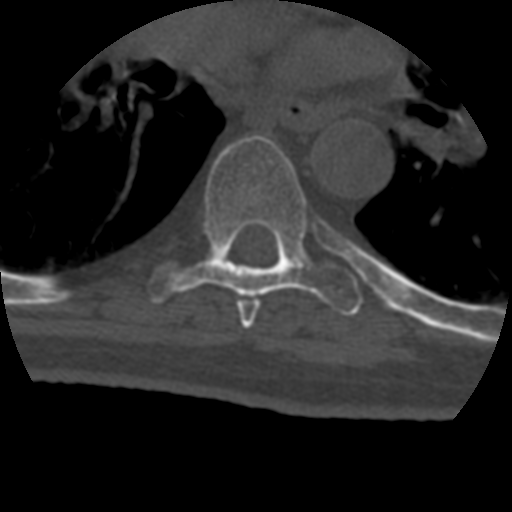
CT including the spine, one axial slice. Position 284 of 399 along the scan axis. Reconstruction kernel STANDARD. Bone window (W 1800 / L 400 HU). 512 × 512 image matrix. Patient age 69 years. Case-level facts recorded for this patient, not image findings: primary cancer: prostate.
Annotated regions visible in this slice (semi-automatic segmentation, software-assisted and operator-edited):
- T6 vertebra: bounding box (x1, y1, x2, y2) in pixels: (237, 300, 259, 329)
- T7 vertebra: (148, 136, 363, 316)